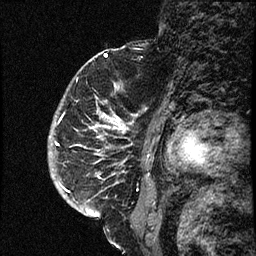
Breast MRI (dynamic contrast-enhanced), one sagittal slice. Slice 51 of 66 in the series (ordered by position). Dynamic contrast-enhanced study with each time point stored as its own series, time point 2 of 3 at this slice position (early post-contrast, ordered by acquisition time). 1.5 T. TE 4.2 ms, TR 17.6 ms. 2 mm slice thickness. 256 × 256 image matrix, field of view 200 × 200 mm. Female patient. Case-level facts recorded for this patient, not image findings: setting: breast cancer imaged before/during neoadjuvant chemotherapy; receptor status: HER2-positive.
Outlined on this slice (semi-automatic segmentation, software-assisted and operator-edited):
- analysis volume of interest (the breast-tissue region the enhancement analysis was run in; not a lesion): bounding box <52,69,139,209> (left, top, right, bottom; pixels)
- tumour enhancement mask (voxels above the 100 % enhancement threshold inside the analysis volume of interest): <56,101,134,208>